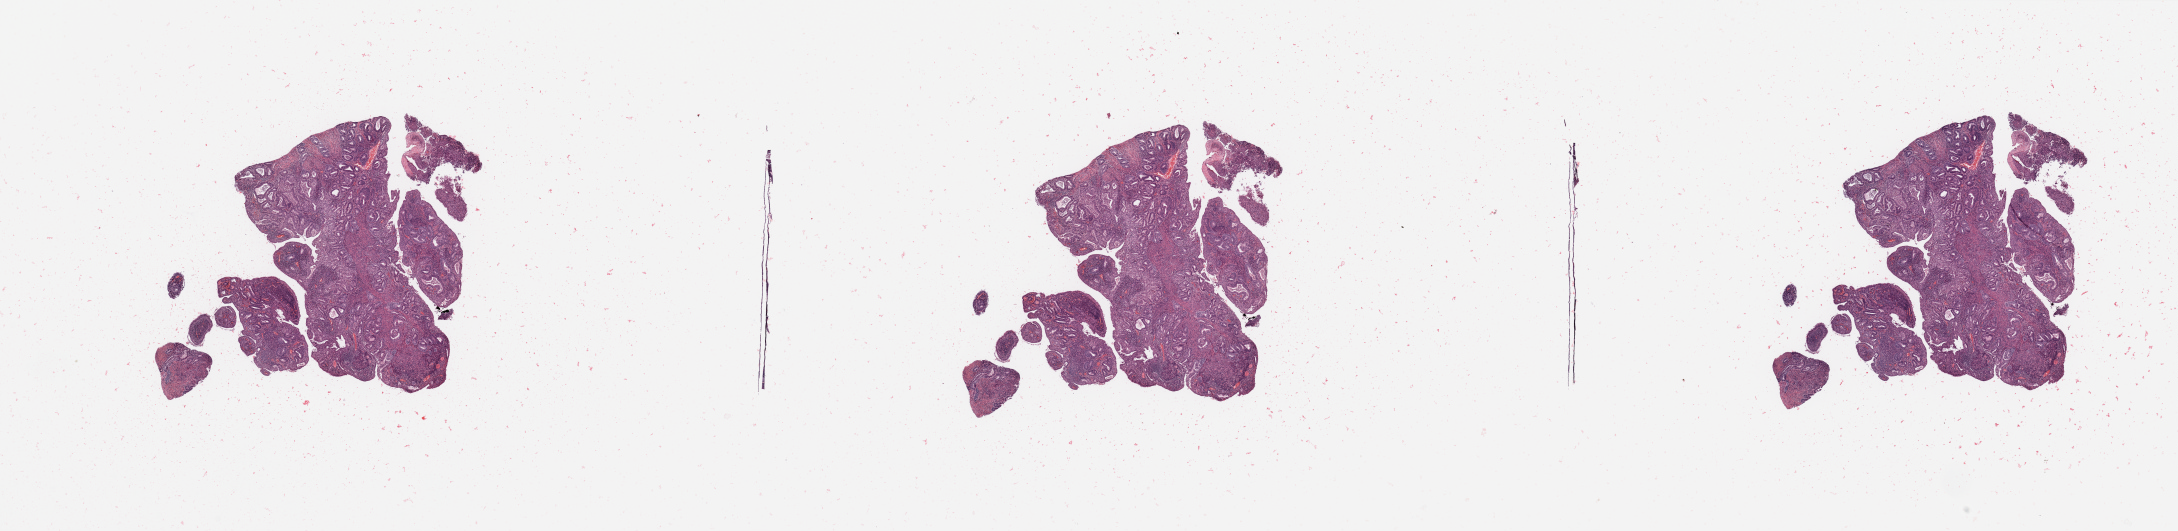
Digitized Hematoxylin and eosin (H&E) stained tissue section (whole slide) — whole scanned area (about 34.5 x 8.4 mm, acquisition: 20x scan) shown as a low-resolution overview; tumour tissue sample, sampled site: uterus. Female, 62 y/o. Histologic grade: G2 (moderately differentiated). Slide review estimates, as recorded: tumour nuclei 80%, necrosis 0%.
Histologic diagnosis: Endometrioid adenocarcinoma, NOS.